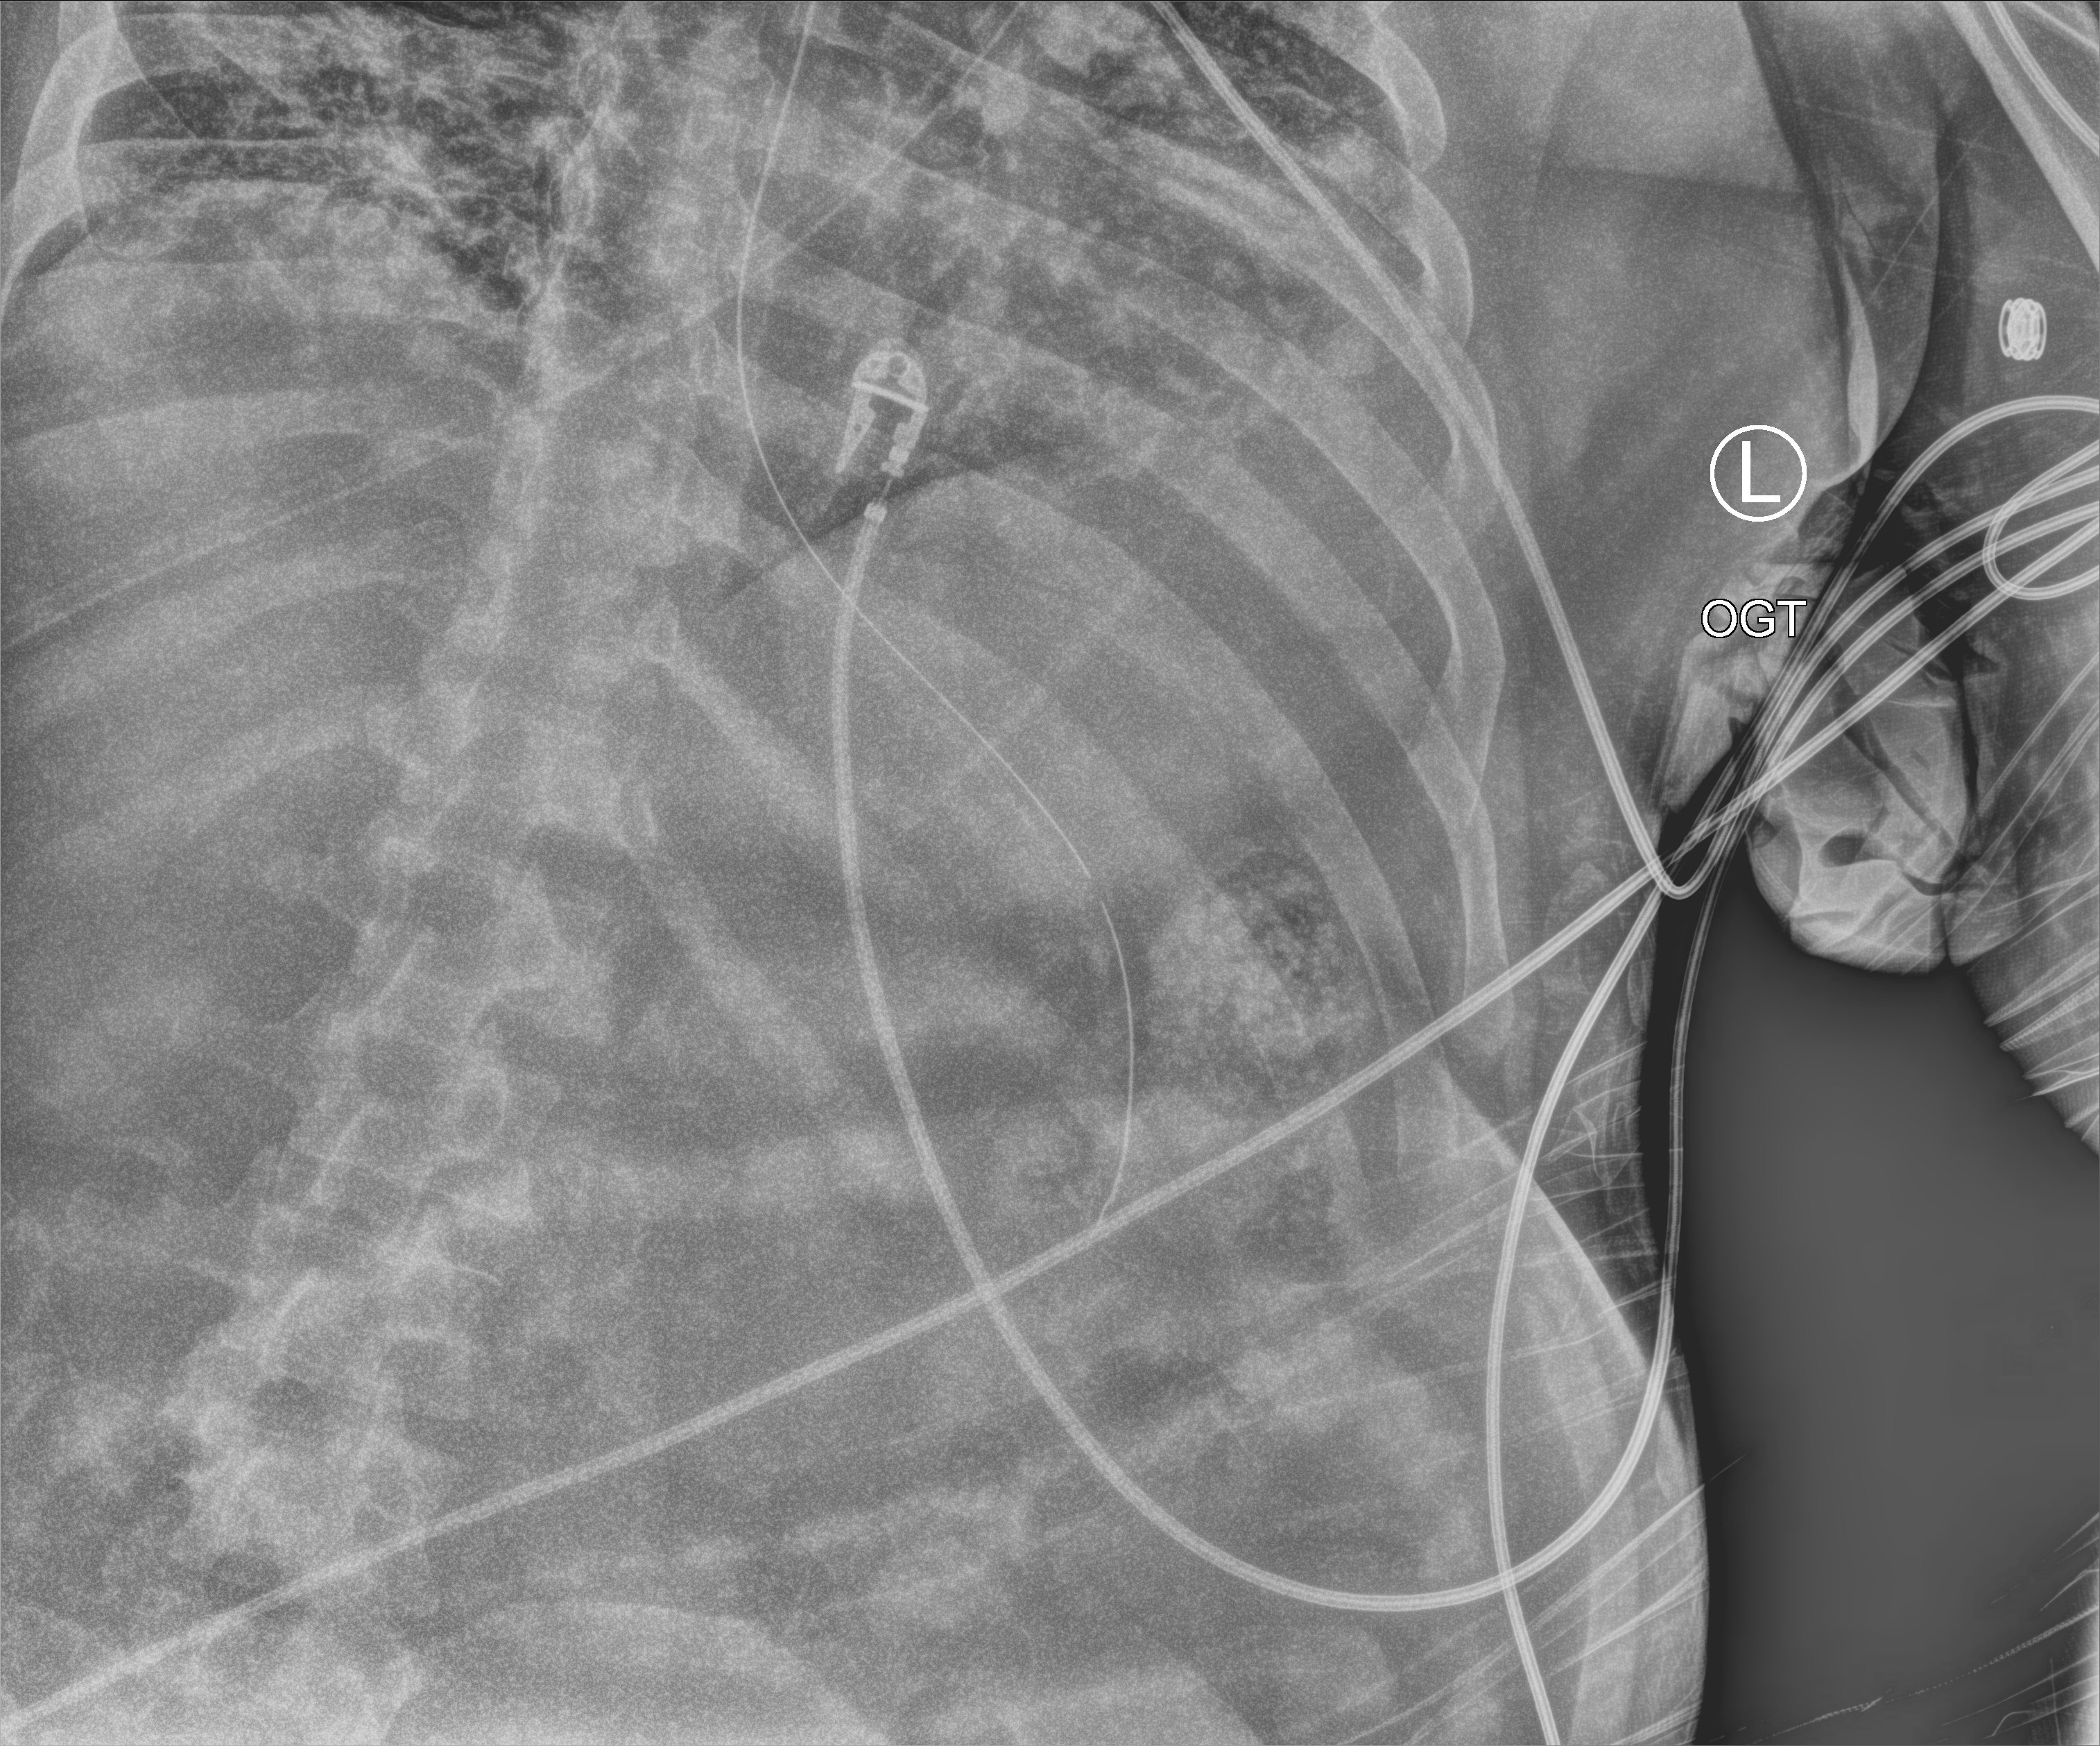
Bedside chest radiograph (computed radiography); anteroposterior (AP) projection. Patient hospitalised with COVID-19; male, aged 18–59 years.
Admission-level facts for this patient (not findings on this image; timing relative to this image not recorded):
- mechanically ventilated during this hospital stay: yes
- other chronic lung disease (admission record): no
- admitted to intensive care during this hospital stay: yes